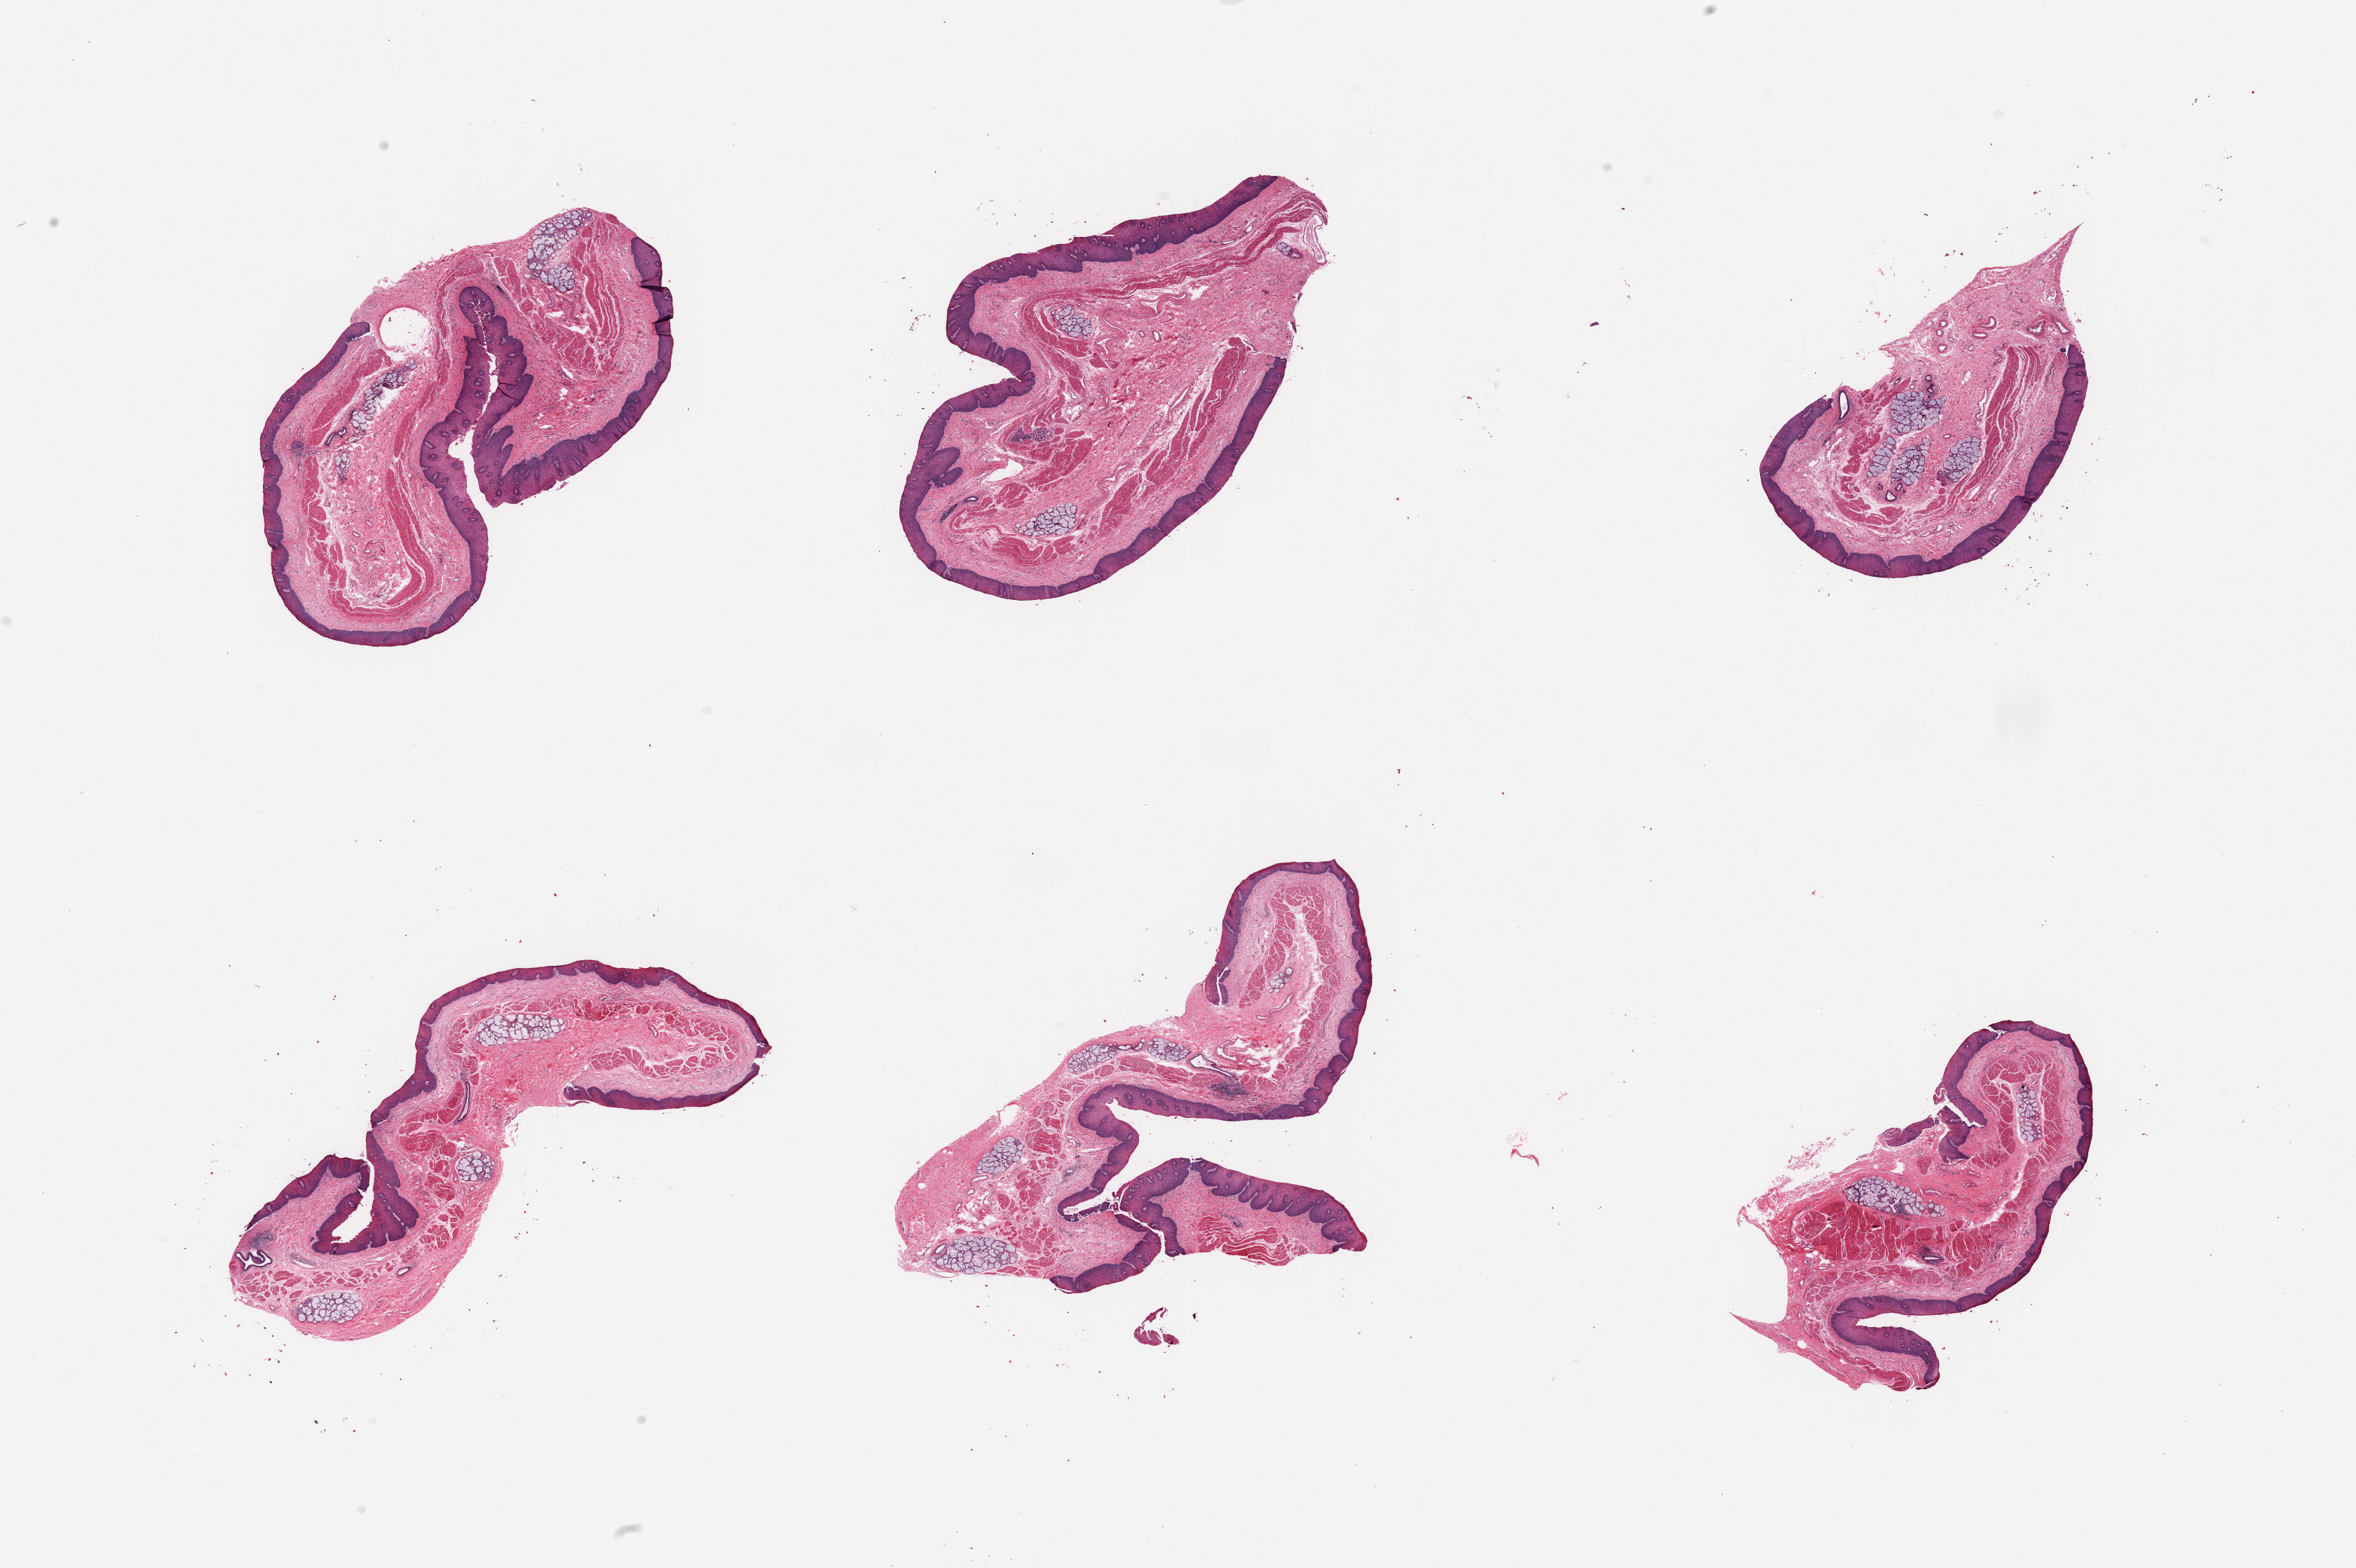
Haematoxylin and eosin whole-slide image, shown as a low-resolution overview of the whole scanned area (about 26.6 x 17.7 mm). PAXgene-fixed paraffin-embedded (PFPE) section. Target tissue: esophageal mucous membrane. Tissue donor sample. Donor: male.
Review note (as recorded): 6 pieces; includes several clusters of submucosal glands.